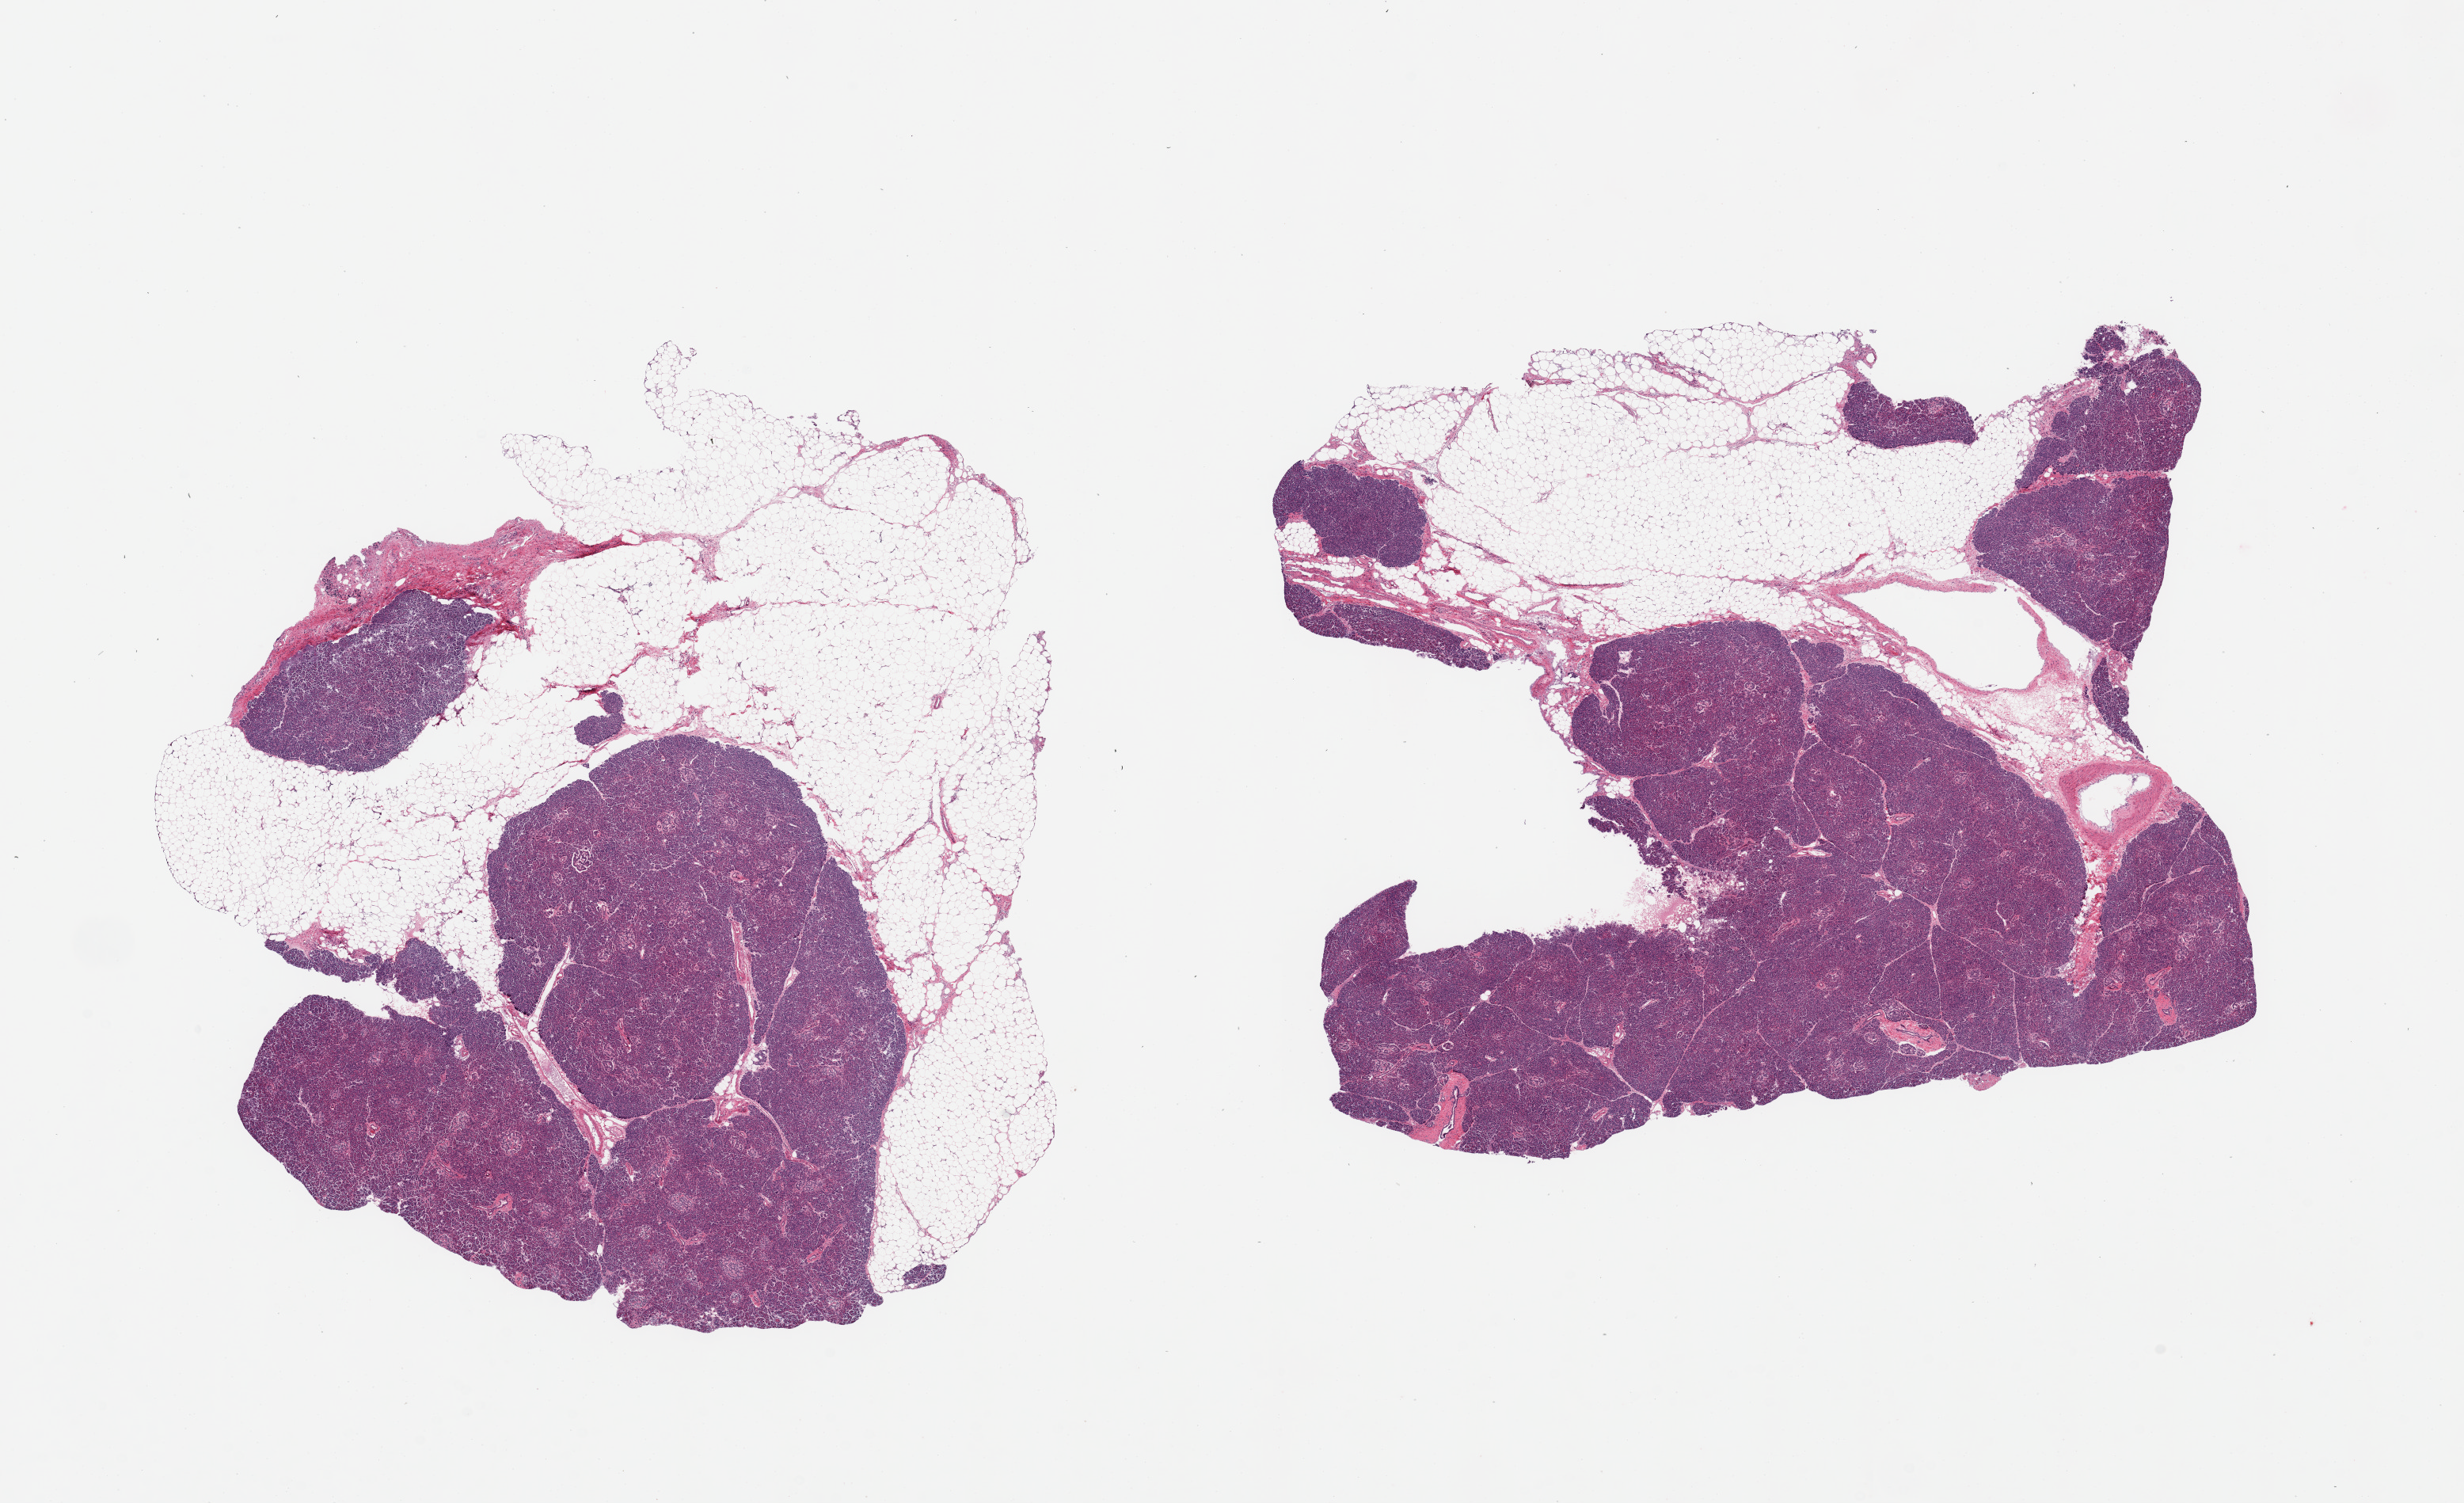
Whole-slide image, H&E stain, shown as a low-resolution overview of the whole scanned area (about 24.6 x 15.0 mm, slide scanned at 20x). PAXgene-fixed, paraffin-embedded tissue. Section of pancreas (target tissue). Donor tissue sample. Donor sex: female.
Reviewer comment on this tissue sample: 2 pieces, 9x8 & 9x7mm; very well preserved; lots of islets; 40-50% adjacent adipose.